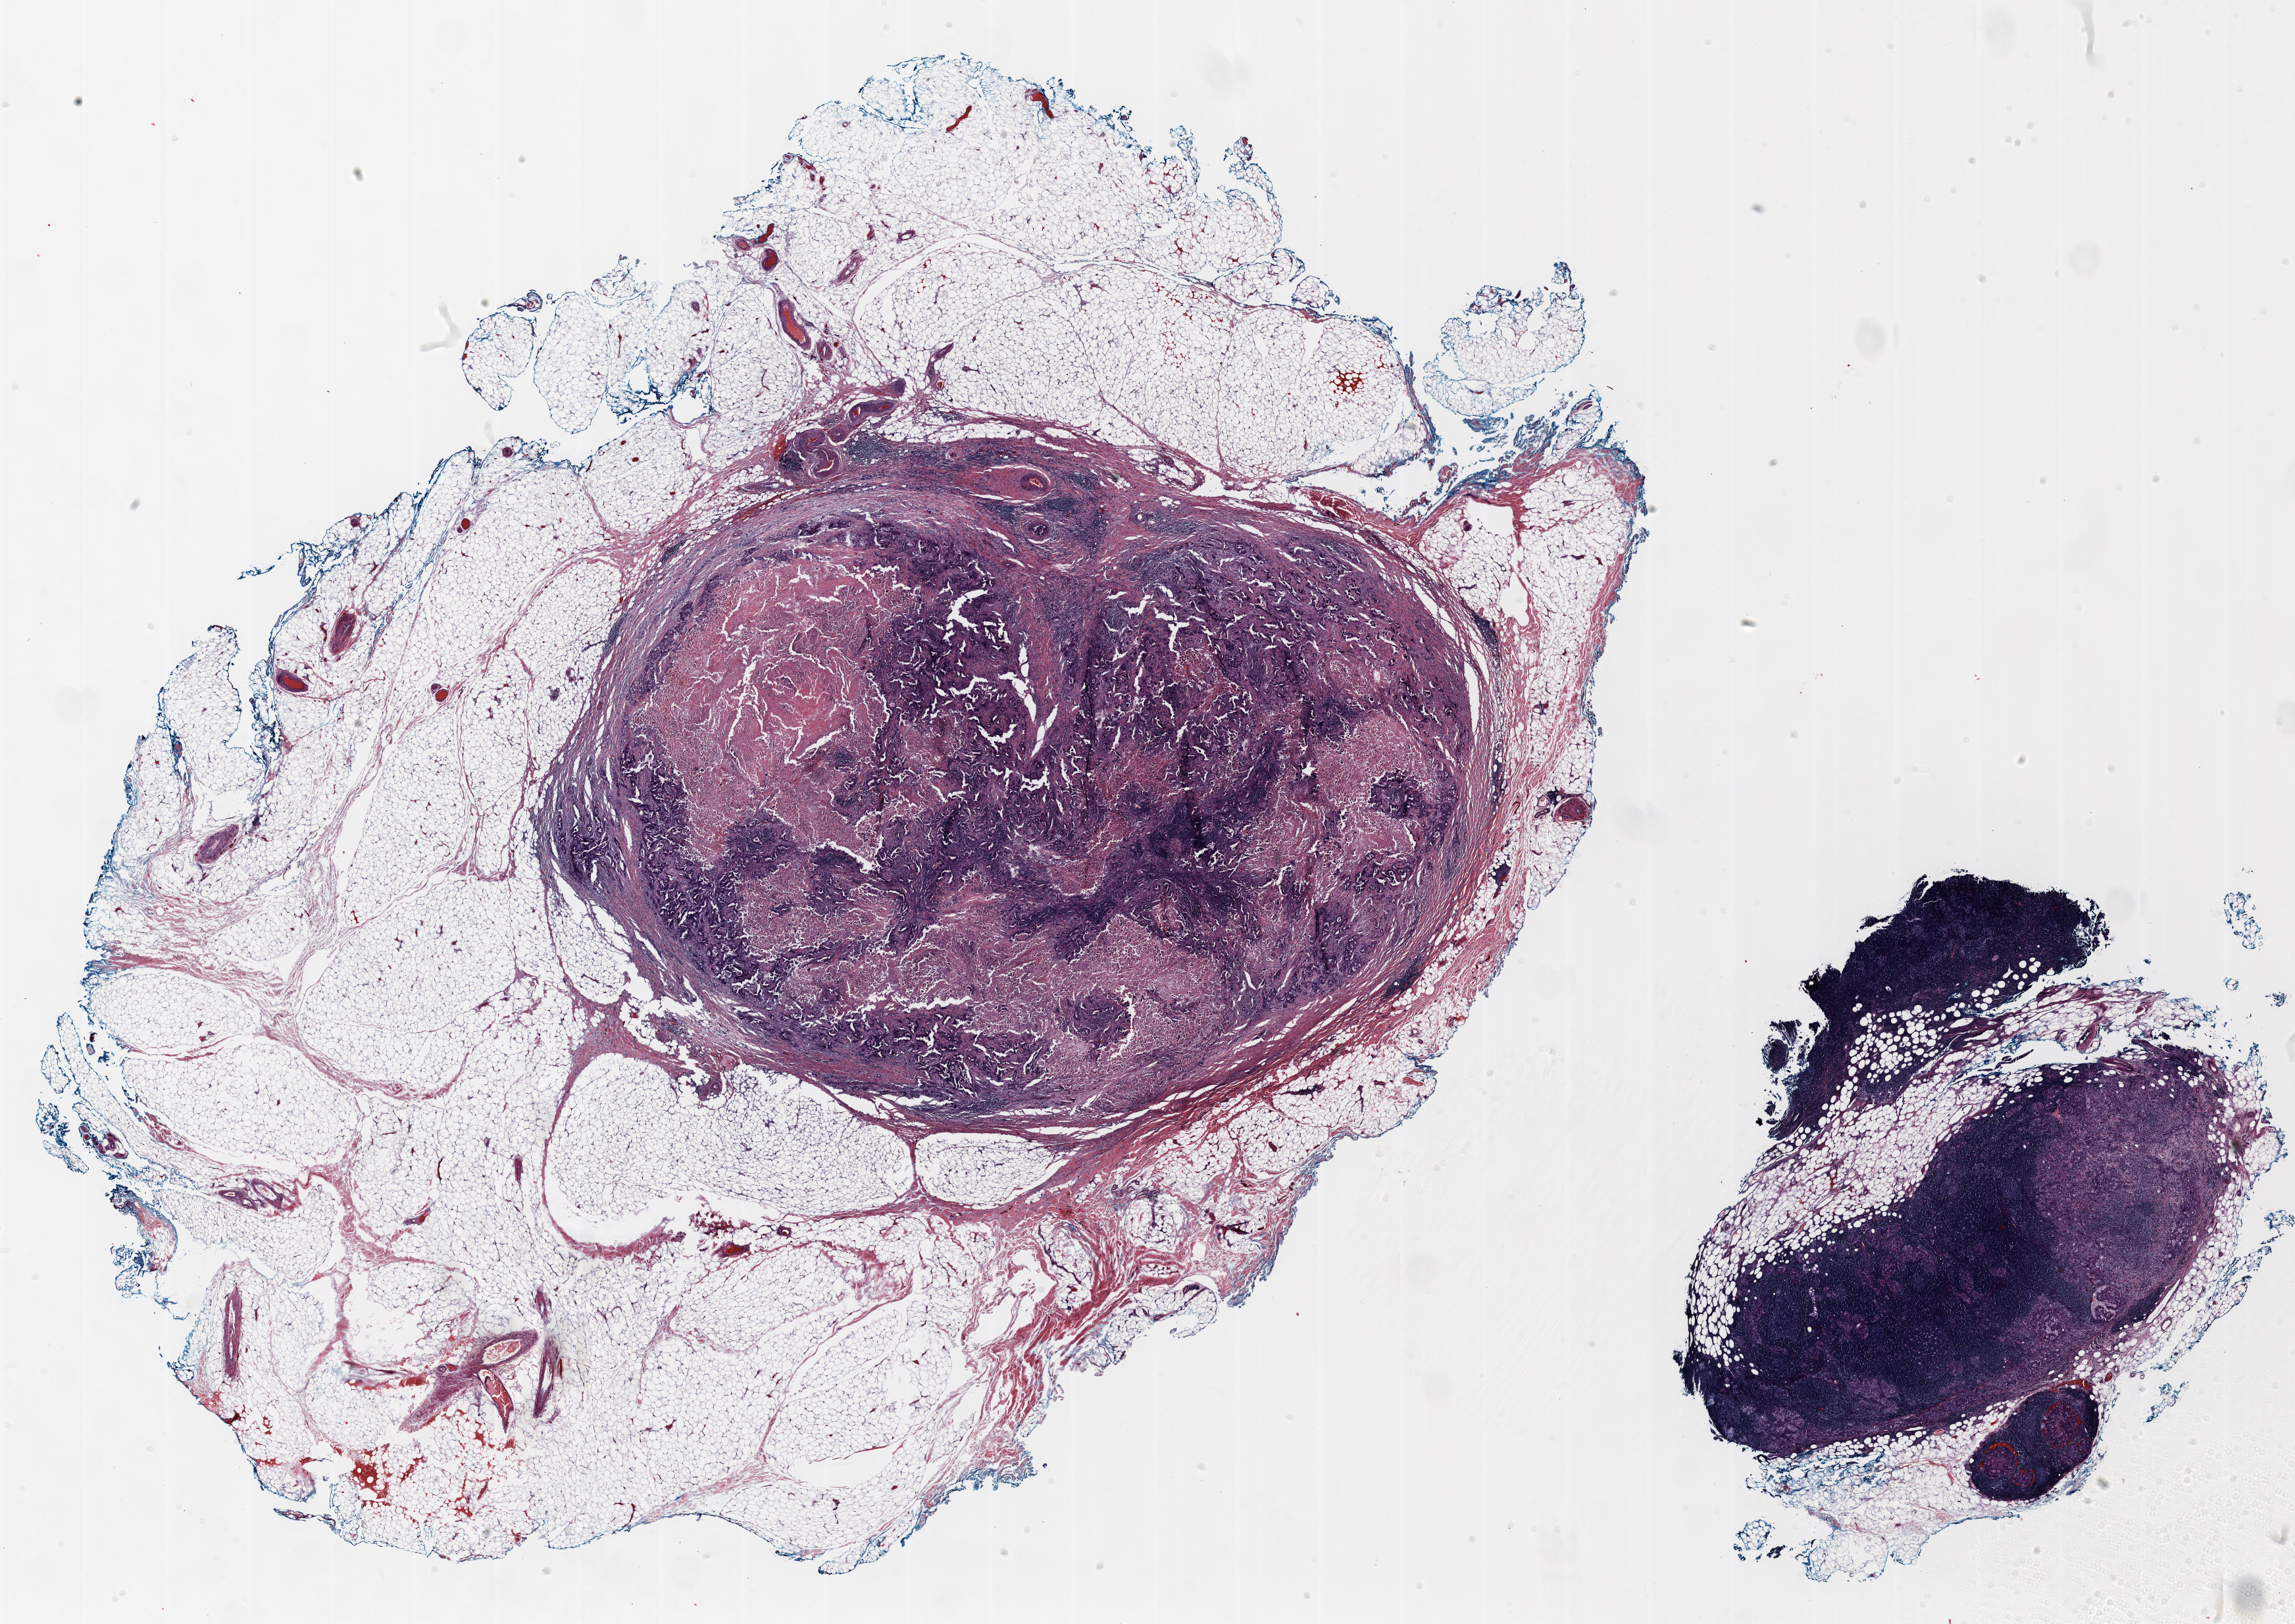
Hematoxylin and eosin (H&E) stained whole-slide image, a low-resolution overview of the entire scanned area, about 28.0 x 19.8 mm (acquisition: 20x scan). FFPE section. Lung. Male, age 67 at enrolment. Former smoker at enrolment. Grade: cannot be assessed (GX).
Tumour size (pathology): 10 mm. Stage (AJCC 6th edition): IIIB. Participant's lung-cancer diagnosis: Adenocarcinoma, NOS (ICD-O-3 8140/3). Primary tumour location (clinical record): left lower lobe.